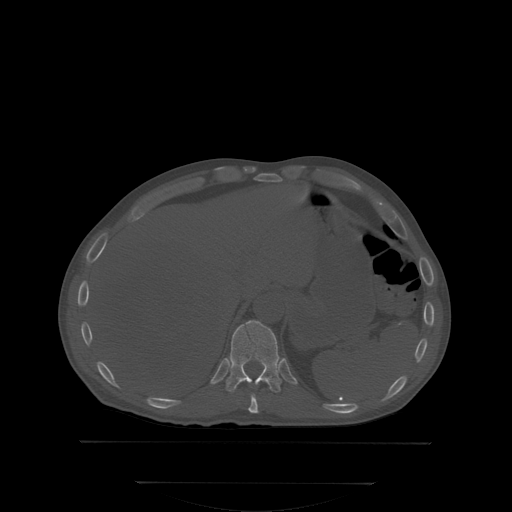
CT including the spine, one axial slice. Position 184 of 350 along the scan axis. Bone window (W 1800 / L 400 HU). 512 × 512 image matrix, field of view 500 × 500 mm. Patient: male, 58 years. From the clinical record (not read from this slice): primary cancer: prostate.
Annotated regions visible in this slice (semi-automatic segmentation, software-assisted and operator-edited):
- T10 vertebra: bounding box (x1, y1, x2, y2) in pixels: (248, 393, 259, 413)
- T11 vertebra: (227, 320, 280, 393)